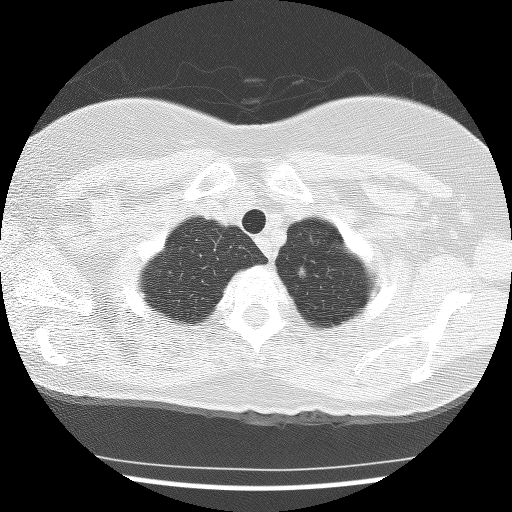
Low-dose screening chest CT, axial slice. Baseline screening round. Lung window (W 1500 / L -600 HU). 2.5 mm slice thickness. Lung (sharp) reconstruction kernel (BONE). Slice 12 of 120 in the series. Female, age 59 years at enrolment.
• Expert-annotated lung lesion, box from (x=282, y=257) to (x=321, y=293) px.
• The screening reader recorded 3 non-calcified nodules or masses ≥4 mm on this exam (left upper lobe, right upper lobe, right upper lobe); which of them this box marks is not recorded.
• Later outcome: lung cancer diagnosed 867 days after this screen (after the third annual screen) — bronchiolo-alveolar adenocarcinoma, NOS, left upper lobe, well differentiated (G1), stage IA (AJCC 6th edition), 10 mm at pathology.